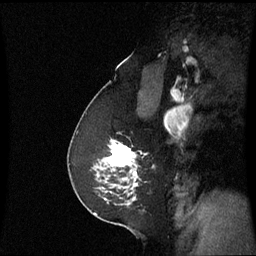
Breast MRI (dynamic contrast-enhanced), one sagittal slice. Slice 41 of 60 in the series (ordered by position). Dynamic contrast-enhanced series, image 2 of 3 at this slice position (ordered by acquisition). 1.5 T. TE 4.2 ms, TR 8.9 ms. 2.2 mm slice thickness. 256 × 256 image matrix, field of view 220 × 220 mm. Female patient, age 58 years. Case-level facts recorded for this patient, not image findings: setting: breast cancer imaged before/during neoadjuvant chemotherapy; receptor status: triple-negative.
Structures marked on this image (semi-automatic segmentation, software-assisted and operator-edited):
- analysis volume of interest (the breast-tissue region the enhancement analysis was run in; not a lesion): bounding box [x1, y1, x2, y2] px = [92, 140, 139, 193]
- tumour enhancement mask (voxels above the 70 % enhancement threshold inside the analysis volume of interest): [106, 140, 139, 187]